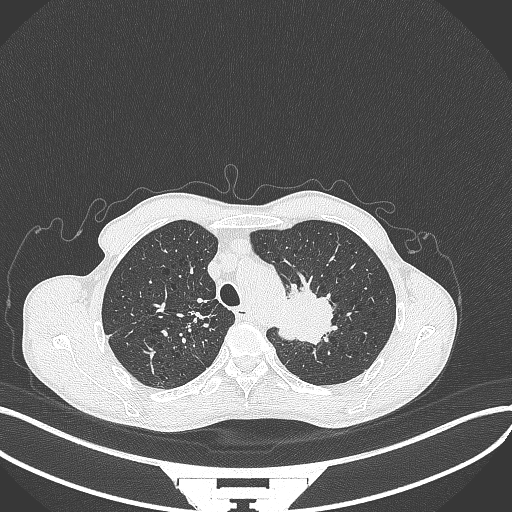
Chest CT, one axial slice. Slice 331 of 386 in the series (ordered by position). Reconstruction kernel B70f. 120 kVp. Lung window (W 1500 / L -600 HU). 512 × 512 image matrix, field of view 400 × 400 mm. Patient: male, 65 years. From the clinical record (not read from this slice): clinical TNM (as recorded): T2b N0 M0.
Annotated regions visible in this slice (bounding box drawn by a radiologist):
- lung tumour (recorded histology: adenocarcinoma): bounding box <273,284,335,346> (left, top, right, bottom; pixels)